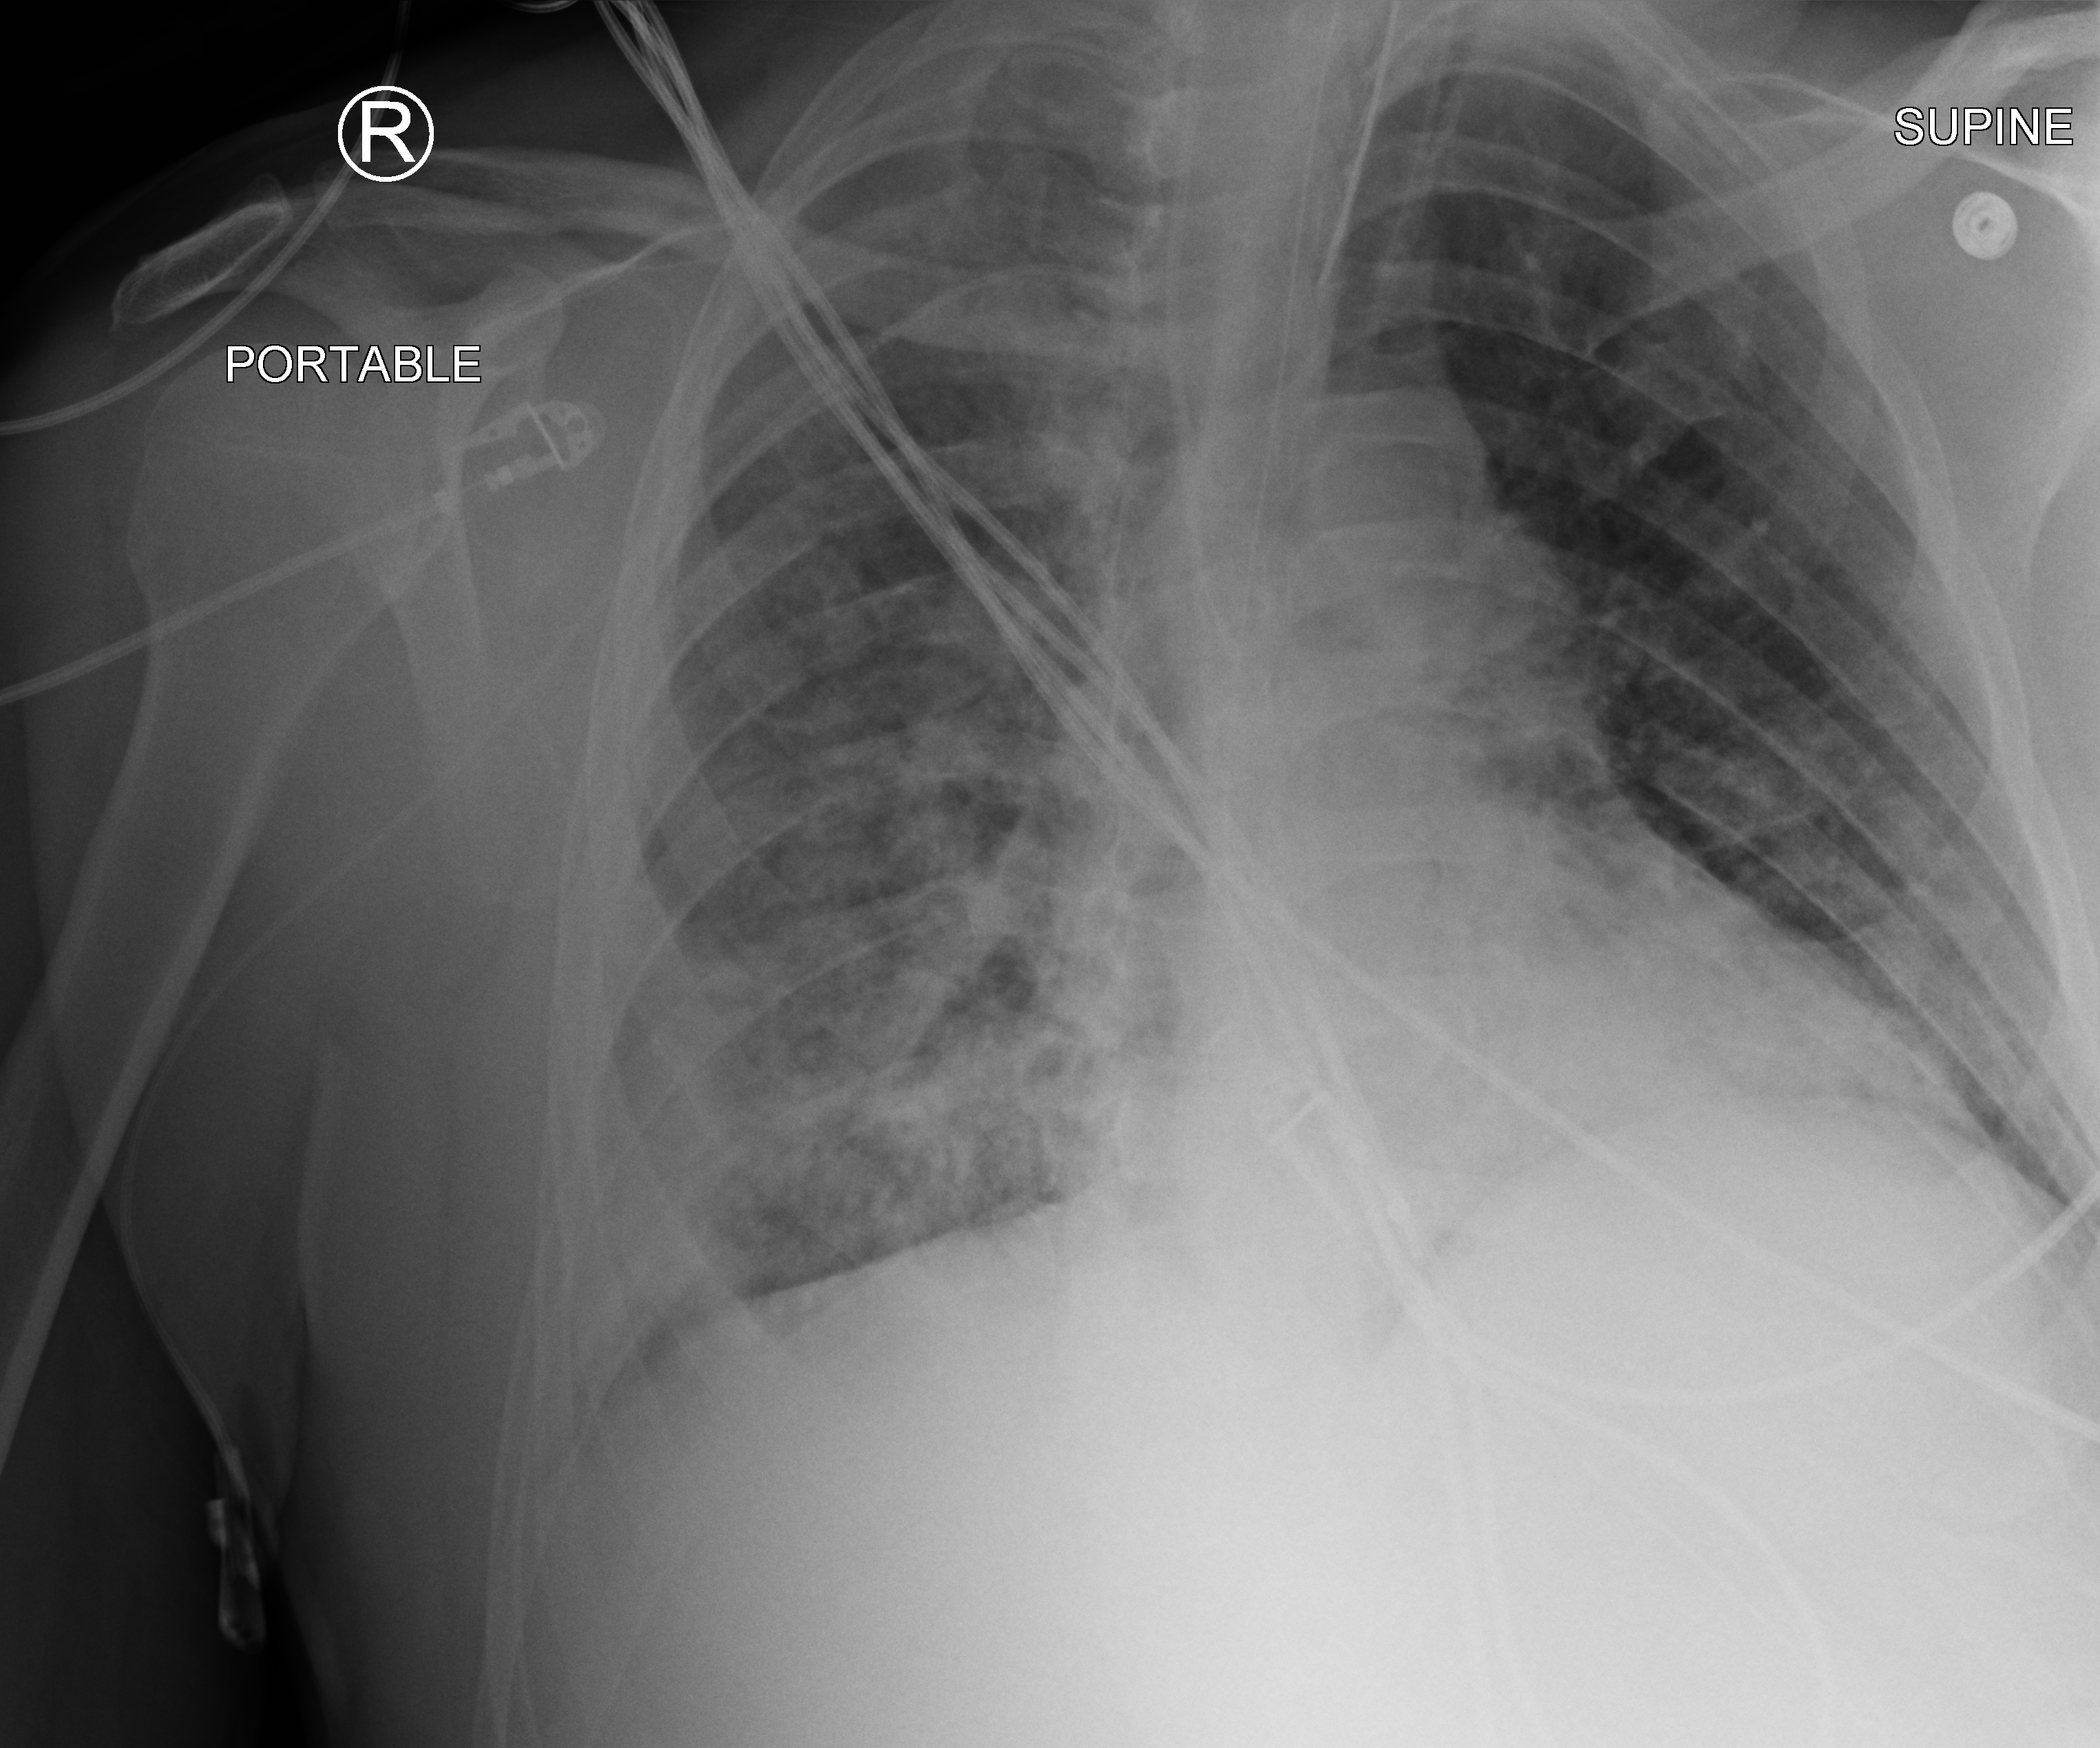
Portable chest radiograph, anteroposterior (AP) projection. Patient hospitalised with COVID-19; male, aged 18–59 years.
Hospital-stay facts (about this admission, not read from this image; timing relative to this image not recorded): admitted to intensive care during this hospital stay: no; mechanically ventilated during this hospital stay: yes.